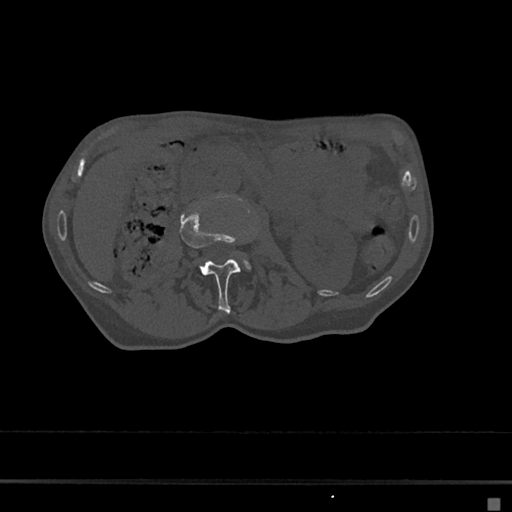
CT including the spine, one axial slice; position 1 of 797 along the scan axis; bone window (W 1800 / L 400 HU); 0.5 mm slice thickness; 512 × 512 image matrix, field of view 360 × 360 mm. Female patient, age 68 years. From the clinical record (not read from this slice): primary cancer: renal.
Outlined on this slice (semi-automatic segmentation, software-assisted and operator-edited):
- L2 vertebra: bounding box [x1, y1, x2, y2] px = [180, 208, 242, 312]